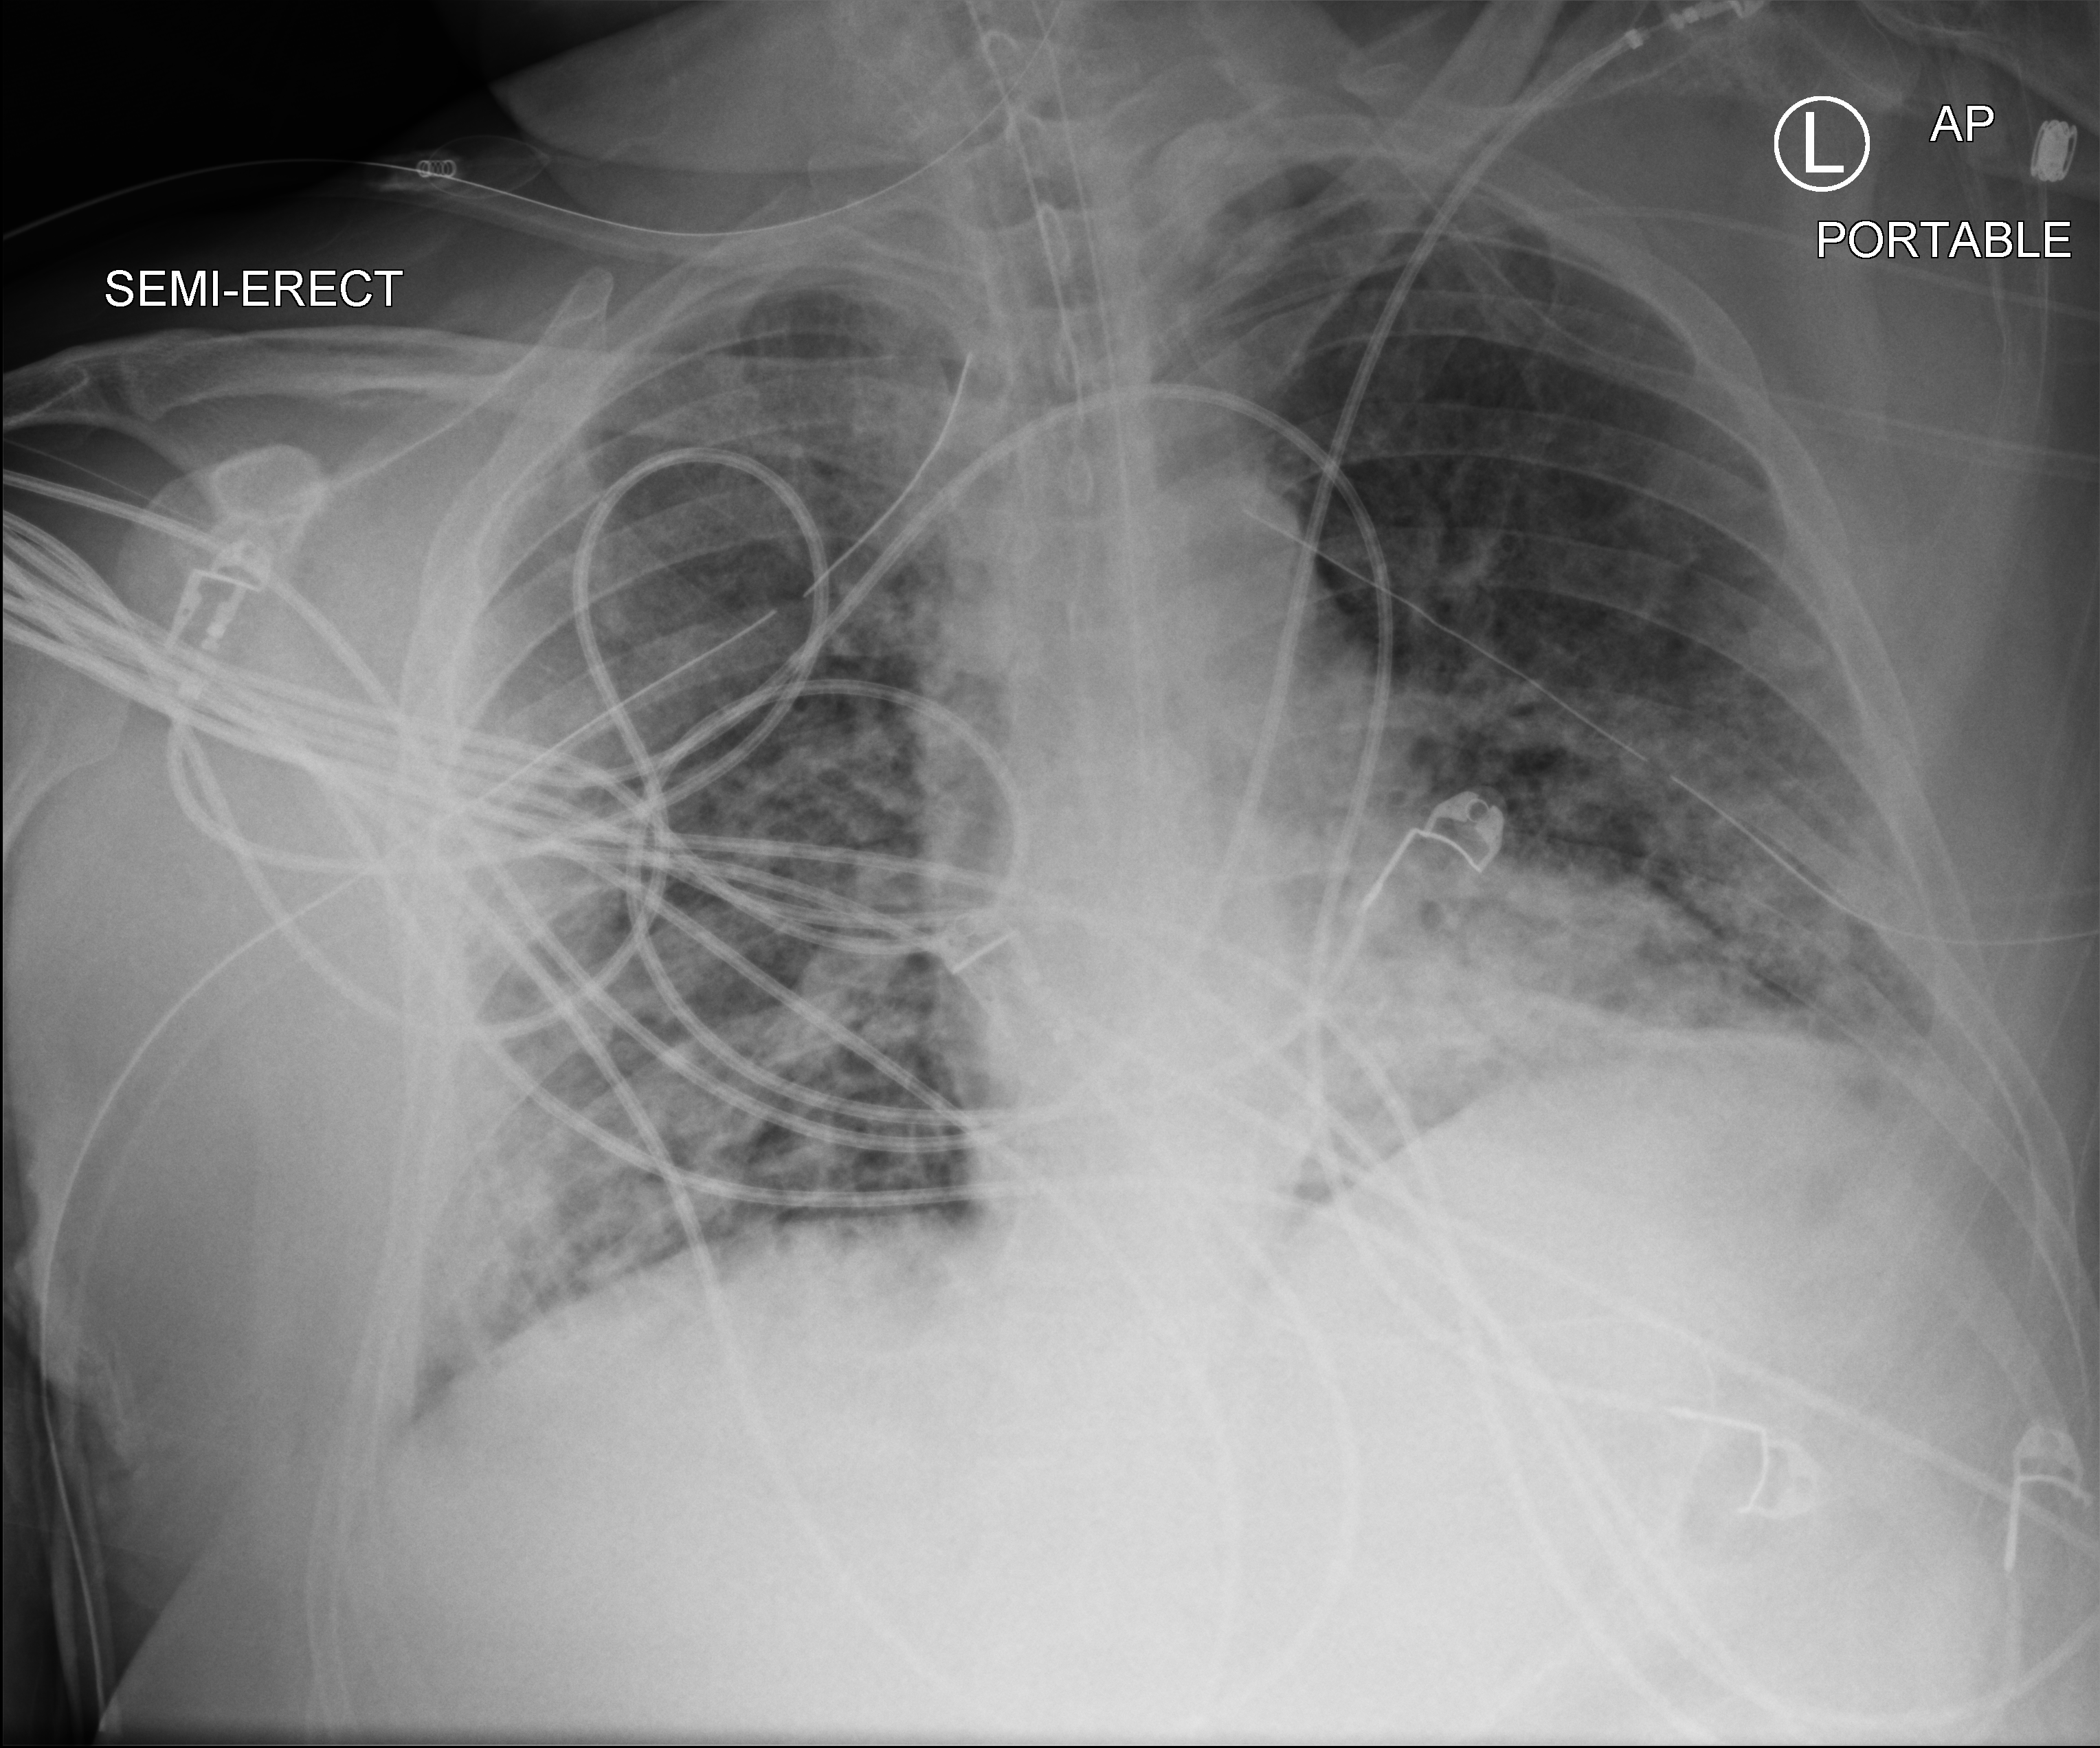
Chest X-ray (portable); anteroposterior (AP) projection. Male patient hospitalised with COVID-19, age 18–59 years.
Hospital-stay facts (about this admission, not read from this image; timing relative to this image not recorded): length of hospital stay: 63 days; diabetes (admission record): yes.